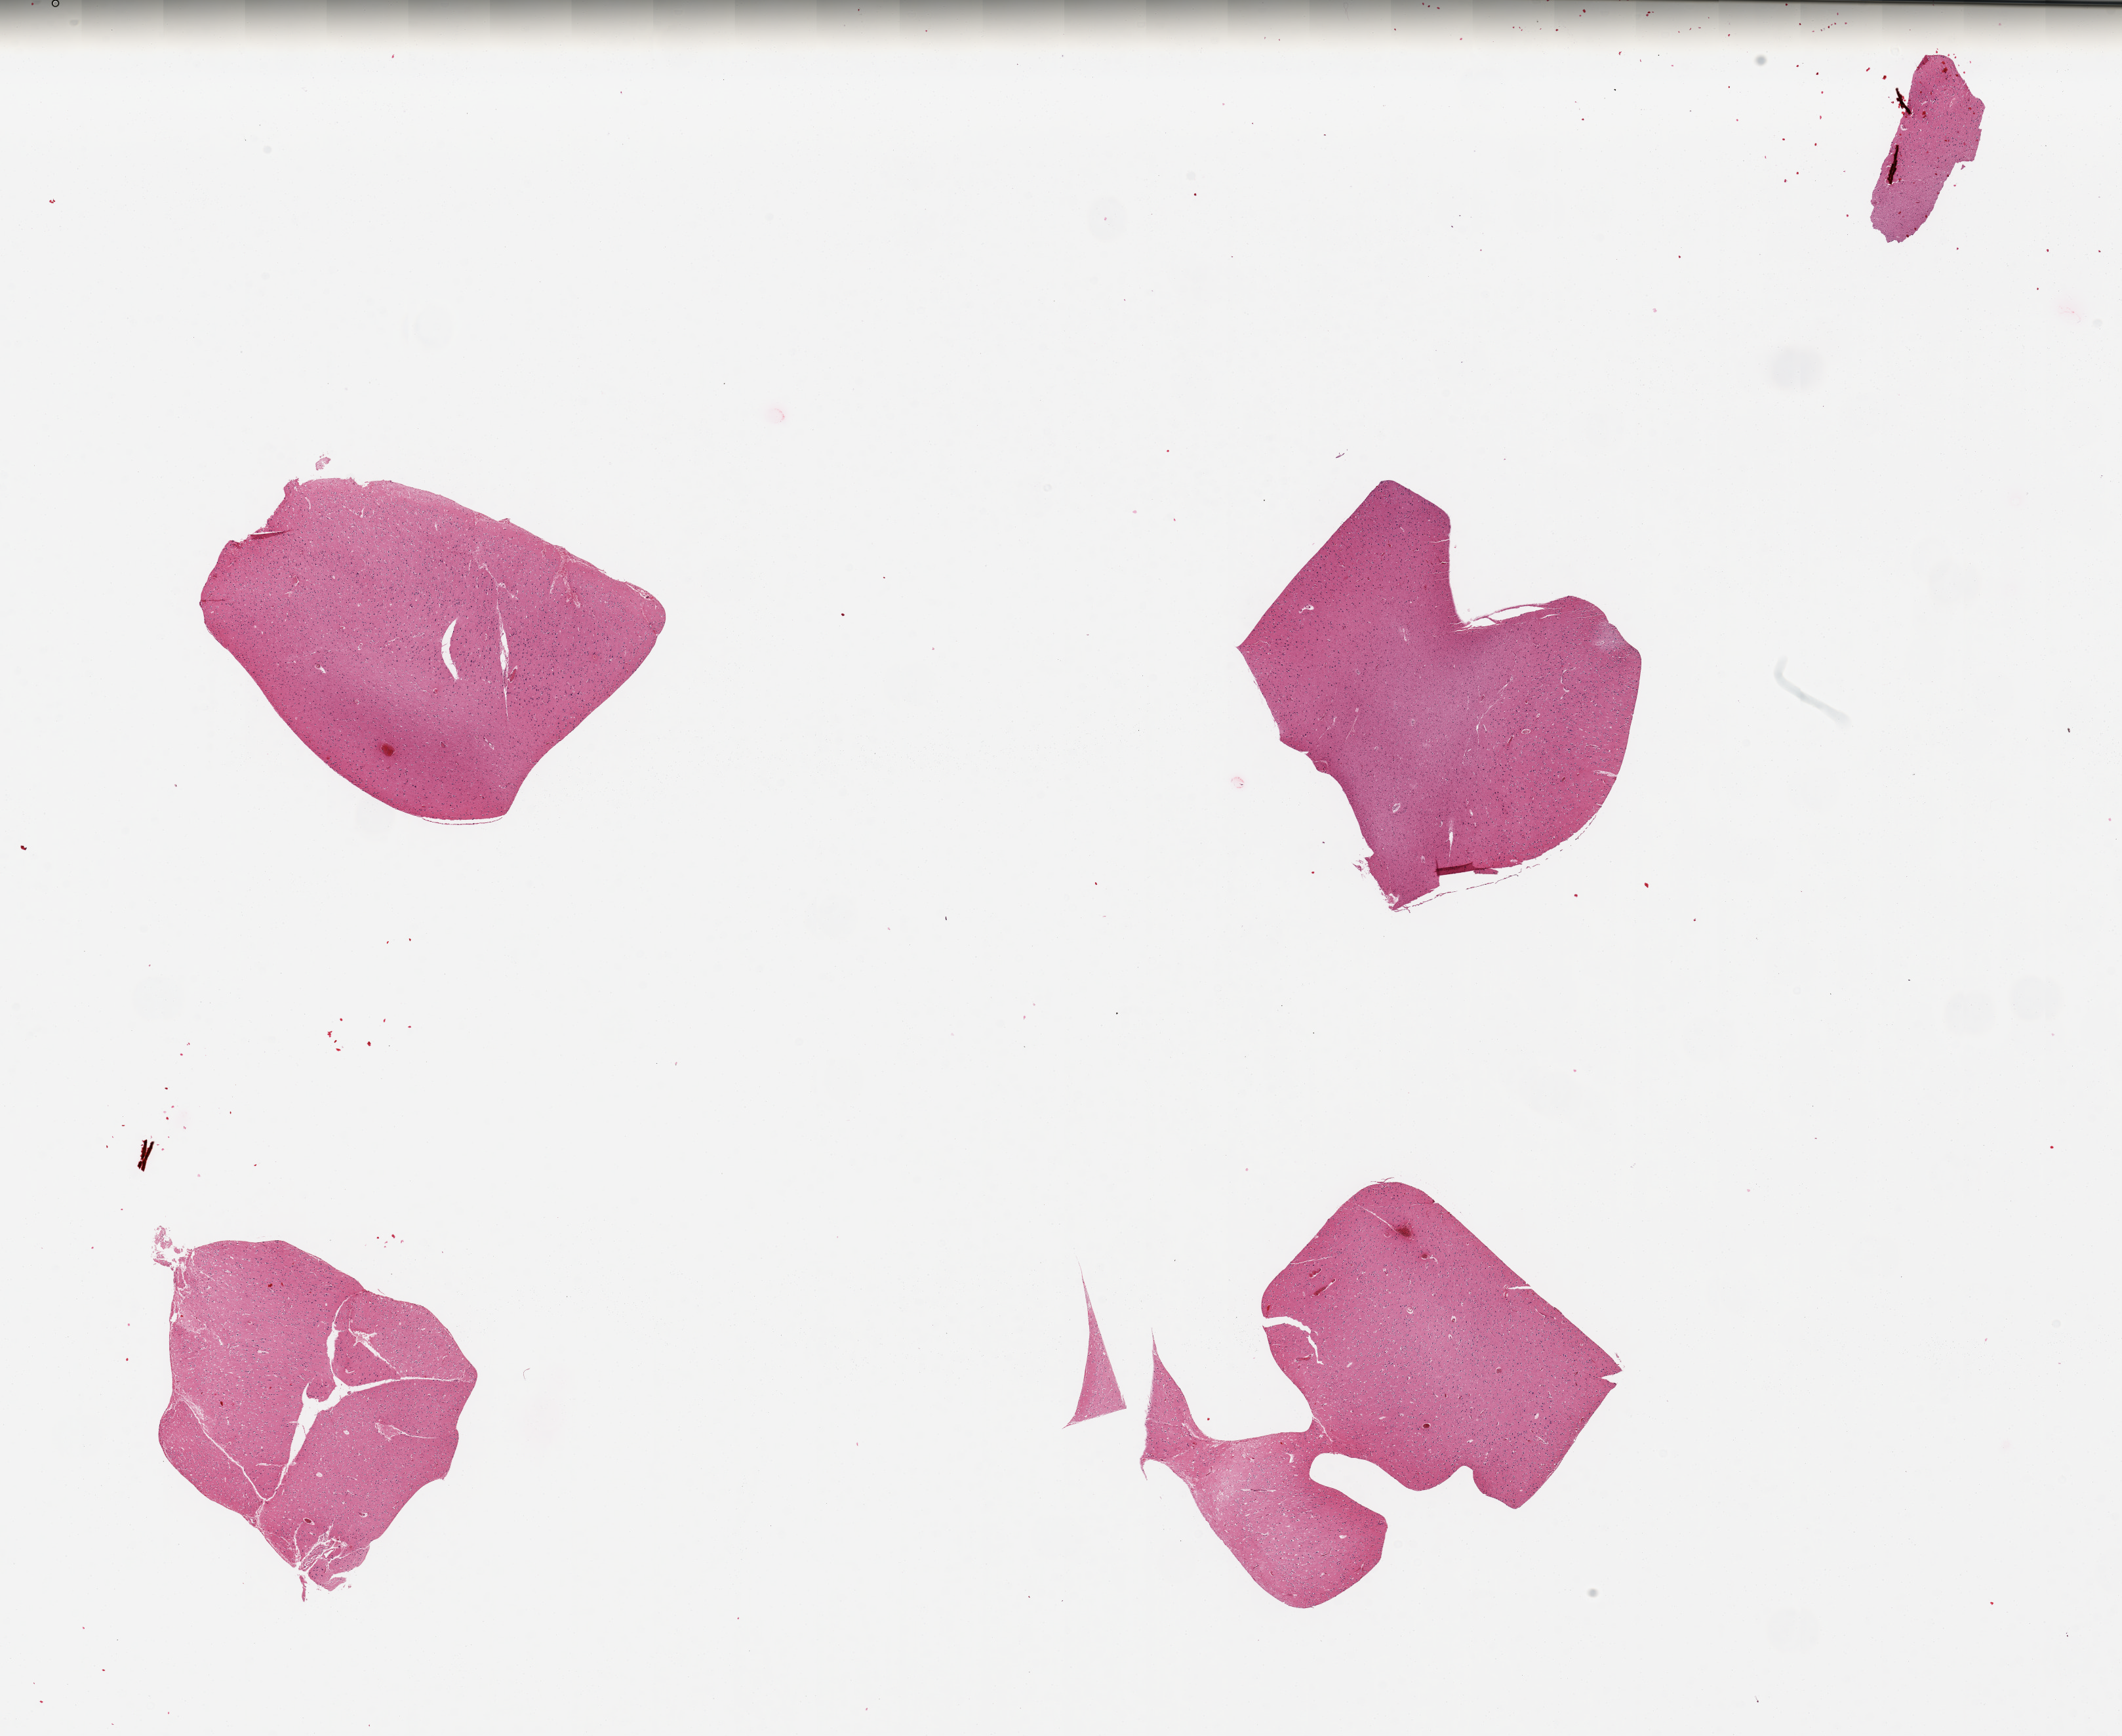
Whole-slide image, H&E stain — shown as a low-resolution overview of the whole scanned area (about 25.6 x 20.9 mm); PAXgene-fixed, paraffin-embedded tissue; target tissue: cerebral cortex; donor tissue sample.
Reviewer comment on this tissue sample: 4 pieces.